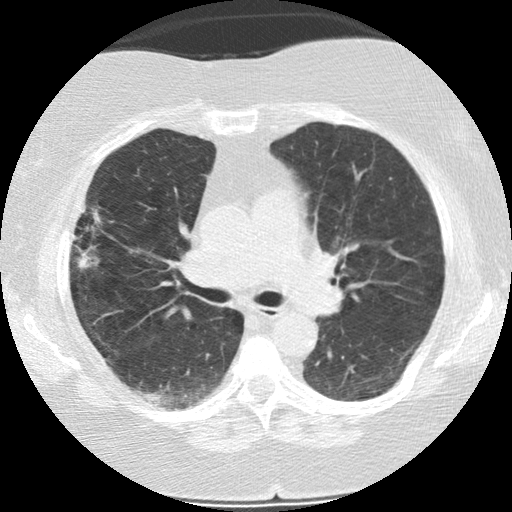
Low-dose screening chest CT, axial slice, baseline screening round, lung window (W 1500 / L -600 HU), 2.5 mm slice thickness, slice 78 of 187 in the series. Female participant, aged 73 years at enrolment.
Lesion marked by an expert reader, bounding box (x1, y1, x2, y2) in pixels: (58, 214, 115, 277). The exam's reader record, not a measurement of the box and not confirmed to be the same lesion: non-calcified nodule or mass ≥4 mm, right upper lobe, 21 × 14 mm, poorly defined margins, soft tissue attenuation. Participant outcome: lung cancer diagnosed 482 days after this screen — bronchiolo-alveolar adenocarcinoma, NOS, right upper lobe, moderately differentiated (G2), stage IIIB (AJCC 6th edition), 21 mm at pathology.